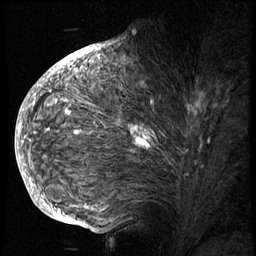
Breast MRI (dynamic contrast-enhanced), one sagittal slice. Slice 42 of 74 in the series (ordered by position). 3 images stored at this slice position (order not interpretable as contrast timing). 1.5 T. TE 4.2 ms, TR 8.9 ms. 256 × 256 image matrix, field of view 200 × 200 mm. Patient: female, 57 years. Case-level facts recorded for this patient, not image findings: setting: breast cancer imaged before/during neoadjuvant chemotherapy; receptor status: HER2-positive.
Outlined on this slice (semi-automatic segmentation, software-assisted and operator-edited):
- analysis volume of interest (the breast-tissue region the enhancement analysis was run in; not a lesion): bounding box <40,62,240,175> (left, top, right, bottom; pixels)
- tumour enhancement mask (voxels above the 140 % enhancement threshold inside the analysis volume of interest): <48,70,199,150>